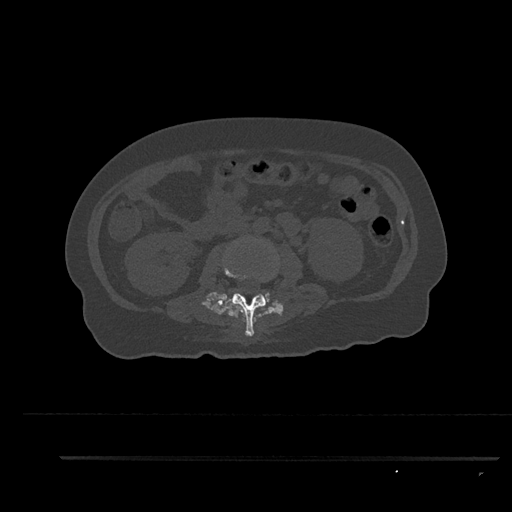
CT including the spine, one axial slice; position 130 of 797 along the scan axis; 120 kVp; bone window (W 1800 / L 400 HU); 512 × 512 image matrix. Female patient, age 44 years. Case-level facts recorded for this patient, not image findings: primary cancer: renal.
Structures marked on this image (semi-automatic segmentation, software-assisted and operator-edited):
- L2 vertebra: bounding box (x1, y1, x2, y2) in pixels: (224, 262, 266, 337)
- L3 vertebra: (225, 292, 276, 303)